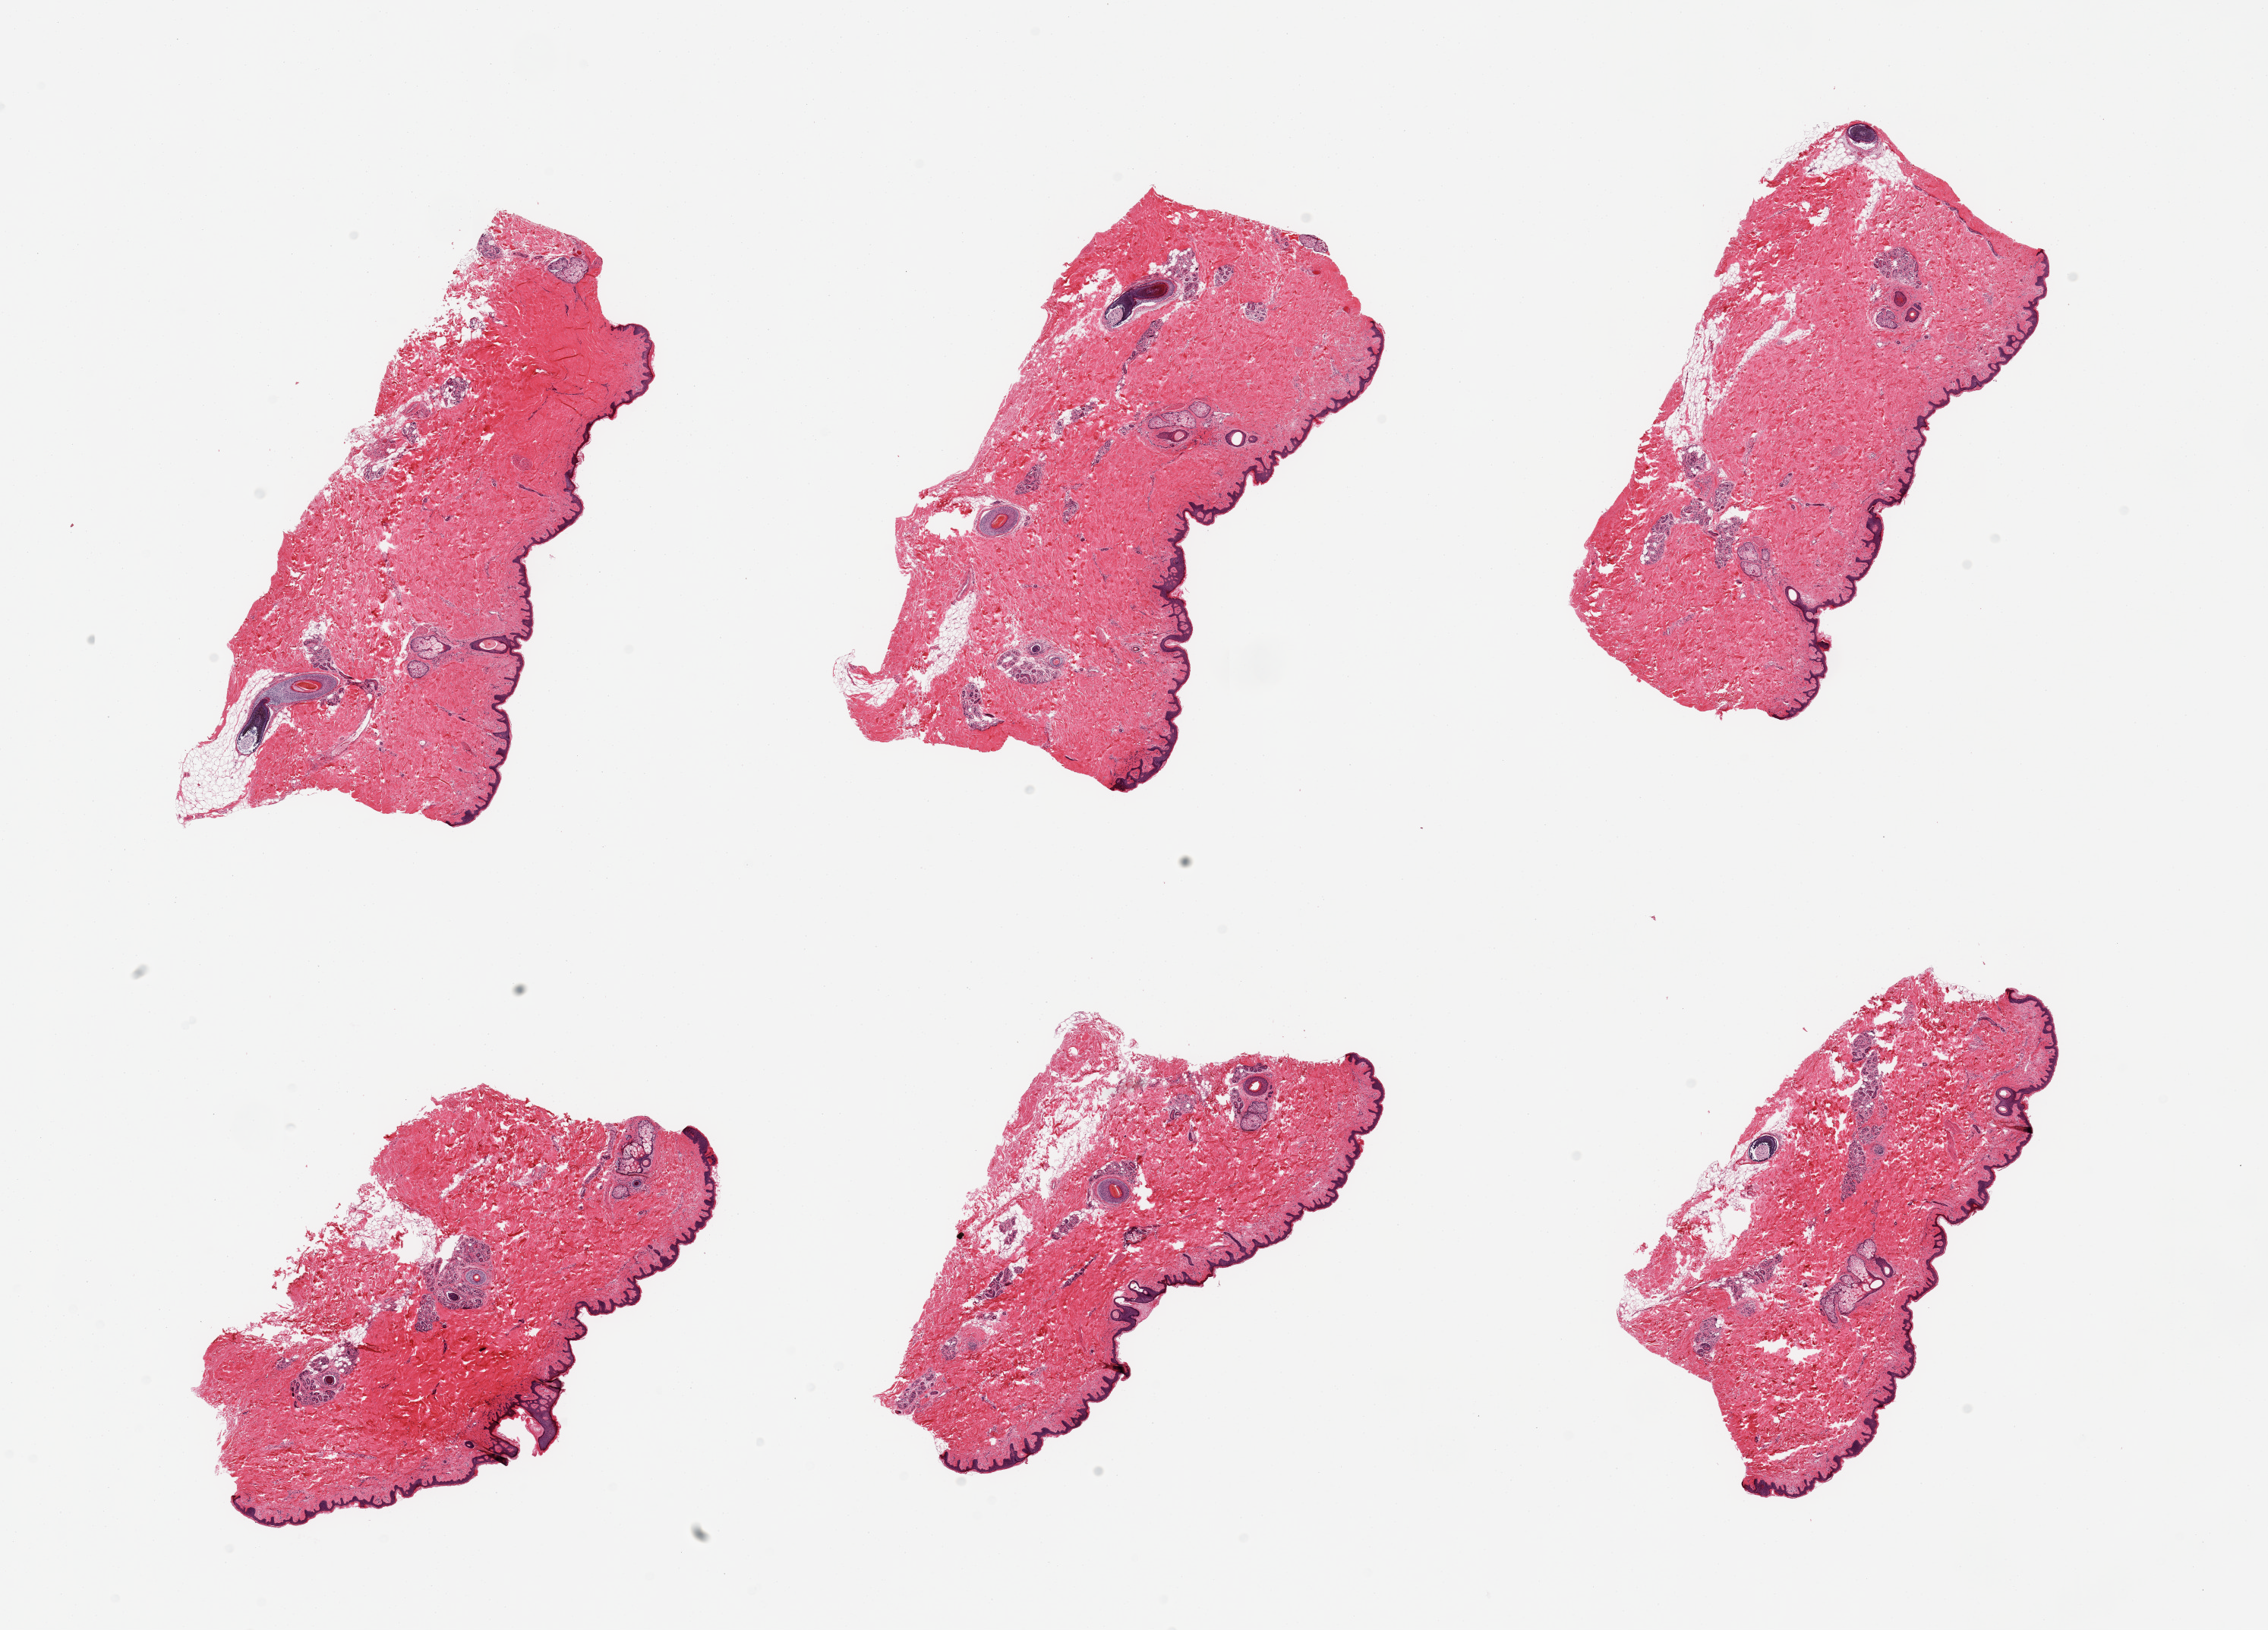
Digitized haematoxylin and eosin-stained section, whole scanned area (about 23.6 x 17.0 mm, acquisition: 20x scan) shown as a low-resolution overview. PAXgene-fixed paraffin-embedded (PFPE) section. Section of skin of suprapubic region (target tissue). Tissue donor sample. Donor: female.
* review note (as recorded): 6 pieces, minimal dermal fat; squamous epithelium is ~40 microns